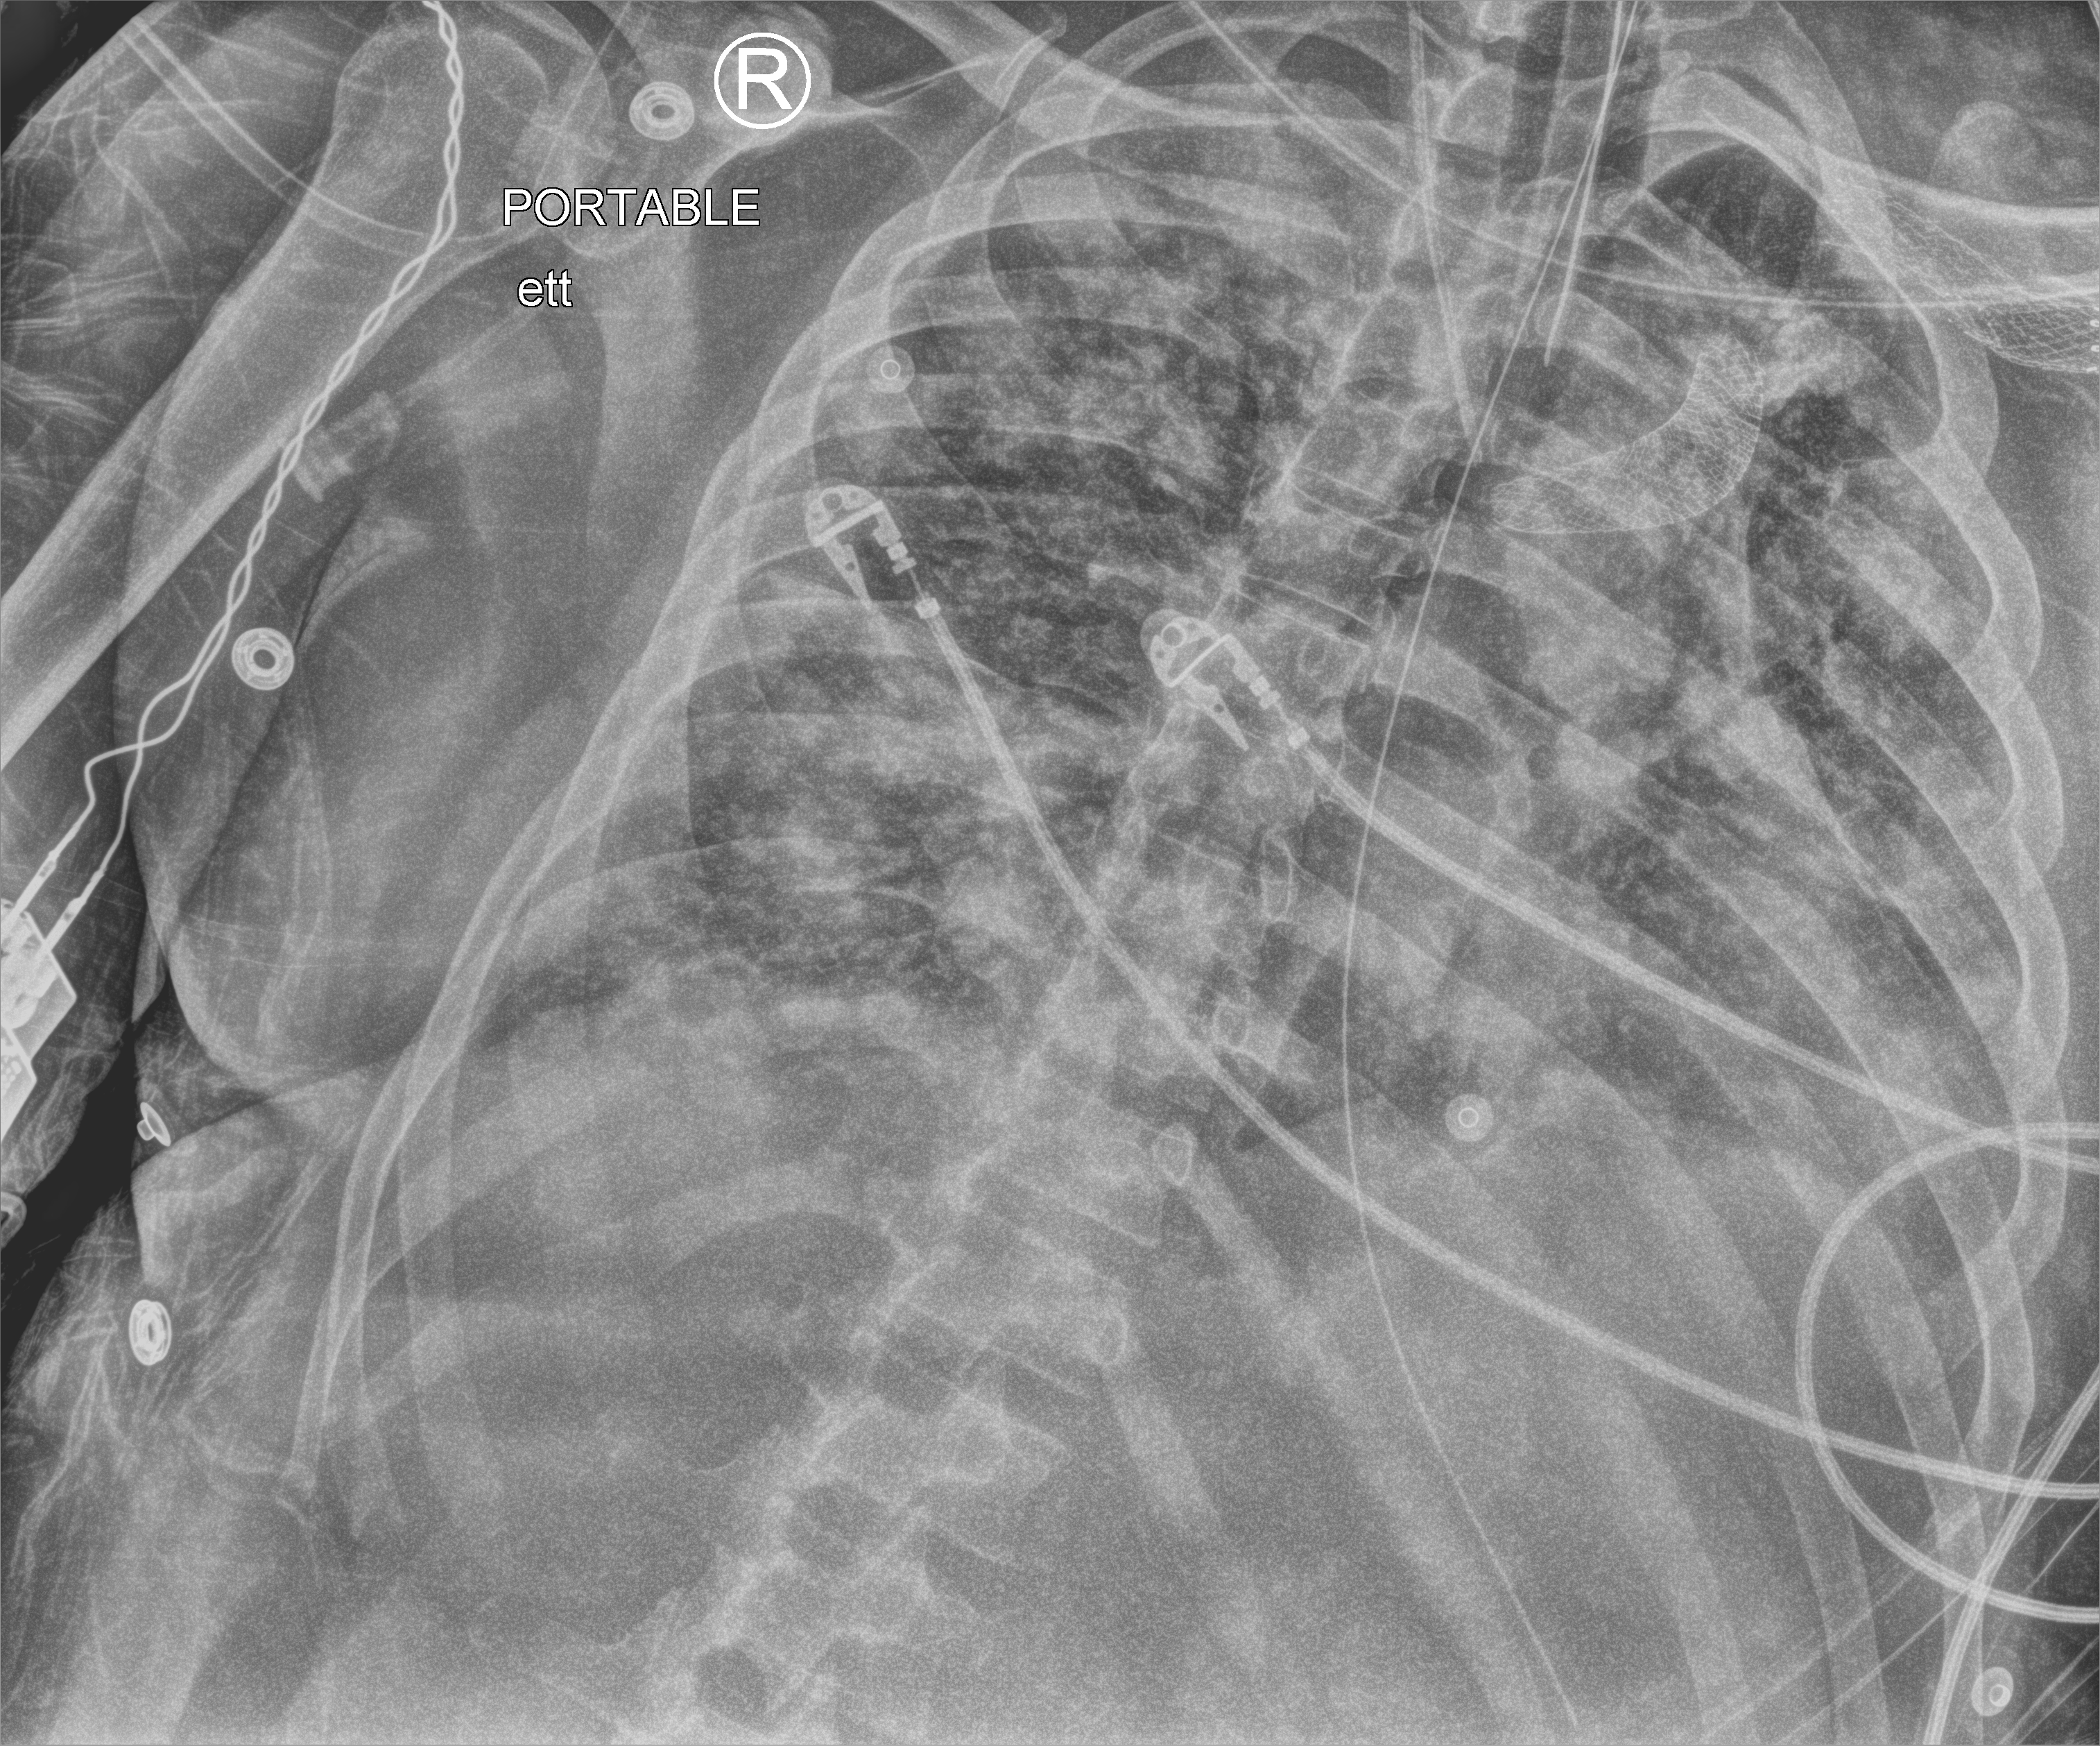
Bedside chest radiograph (computed radiography), anteroposterior (AP) projection. Patient hospitalised with COVID-19; male, aged 18–59 years.
Admission-level facts for this patient (not findings on this image; timing relative to this image not recorded): mechanically ventilated during this hospital stay: yes; diabetes (admission record): no; admitted to intensive care during this hospital stay: yes.